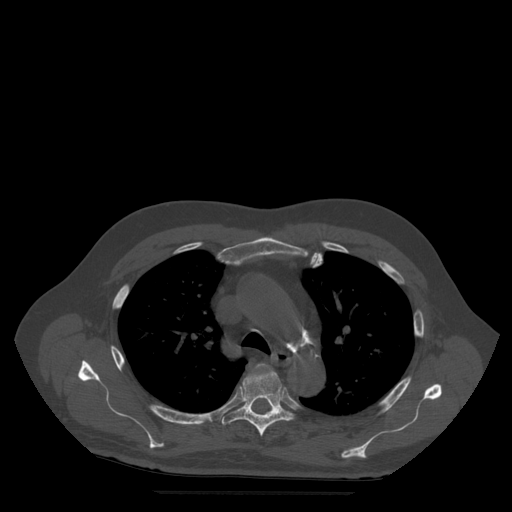
CT including the spine, one axial slice. Slice 375 of 522 in the series (ordered by position). Bone window (W 1800 / L 400 HU). 512 × 512 image matrix, field of view 420 × 420 mm. Patient age 72 years. Case-level facts recorded for this patient, not image findings: primary cancer: prostate.
Outlined on this slice (semi-automatic segmentation, software-assisted and operator-edited):
- T4 vertebra: bounding box [x1, y1, x2, y2] px = [258, 364, 265, 367]
- T5 vertebra: [222, 367, 296, 436]